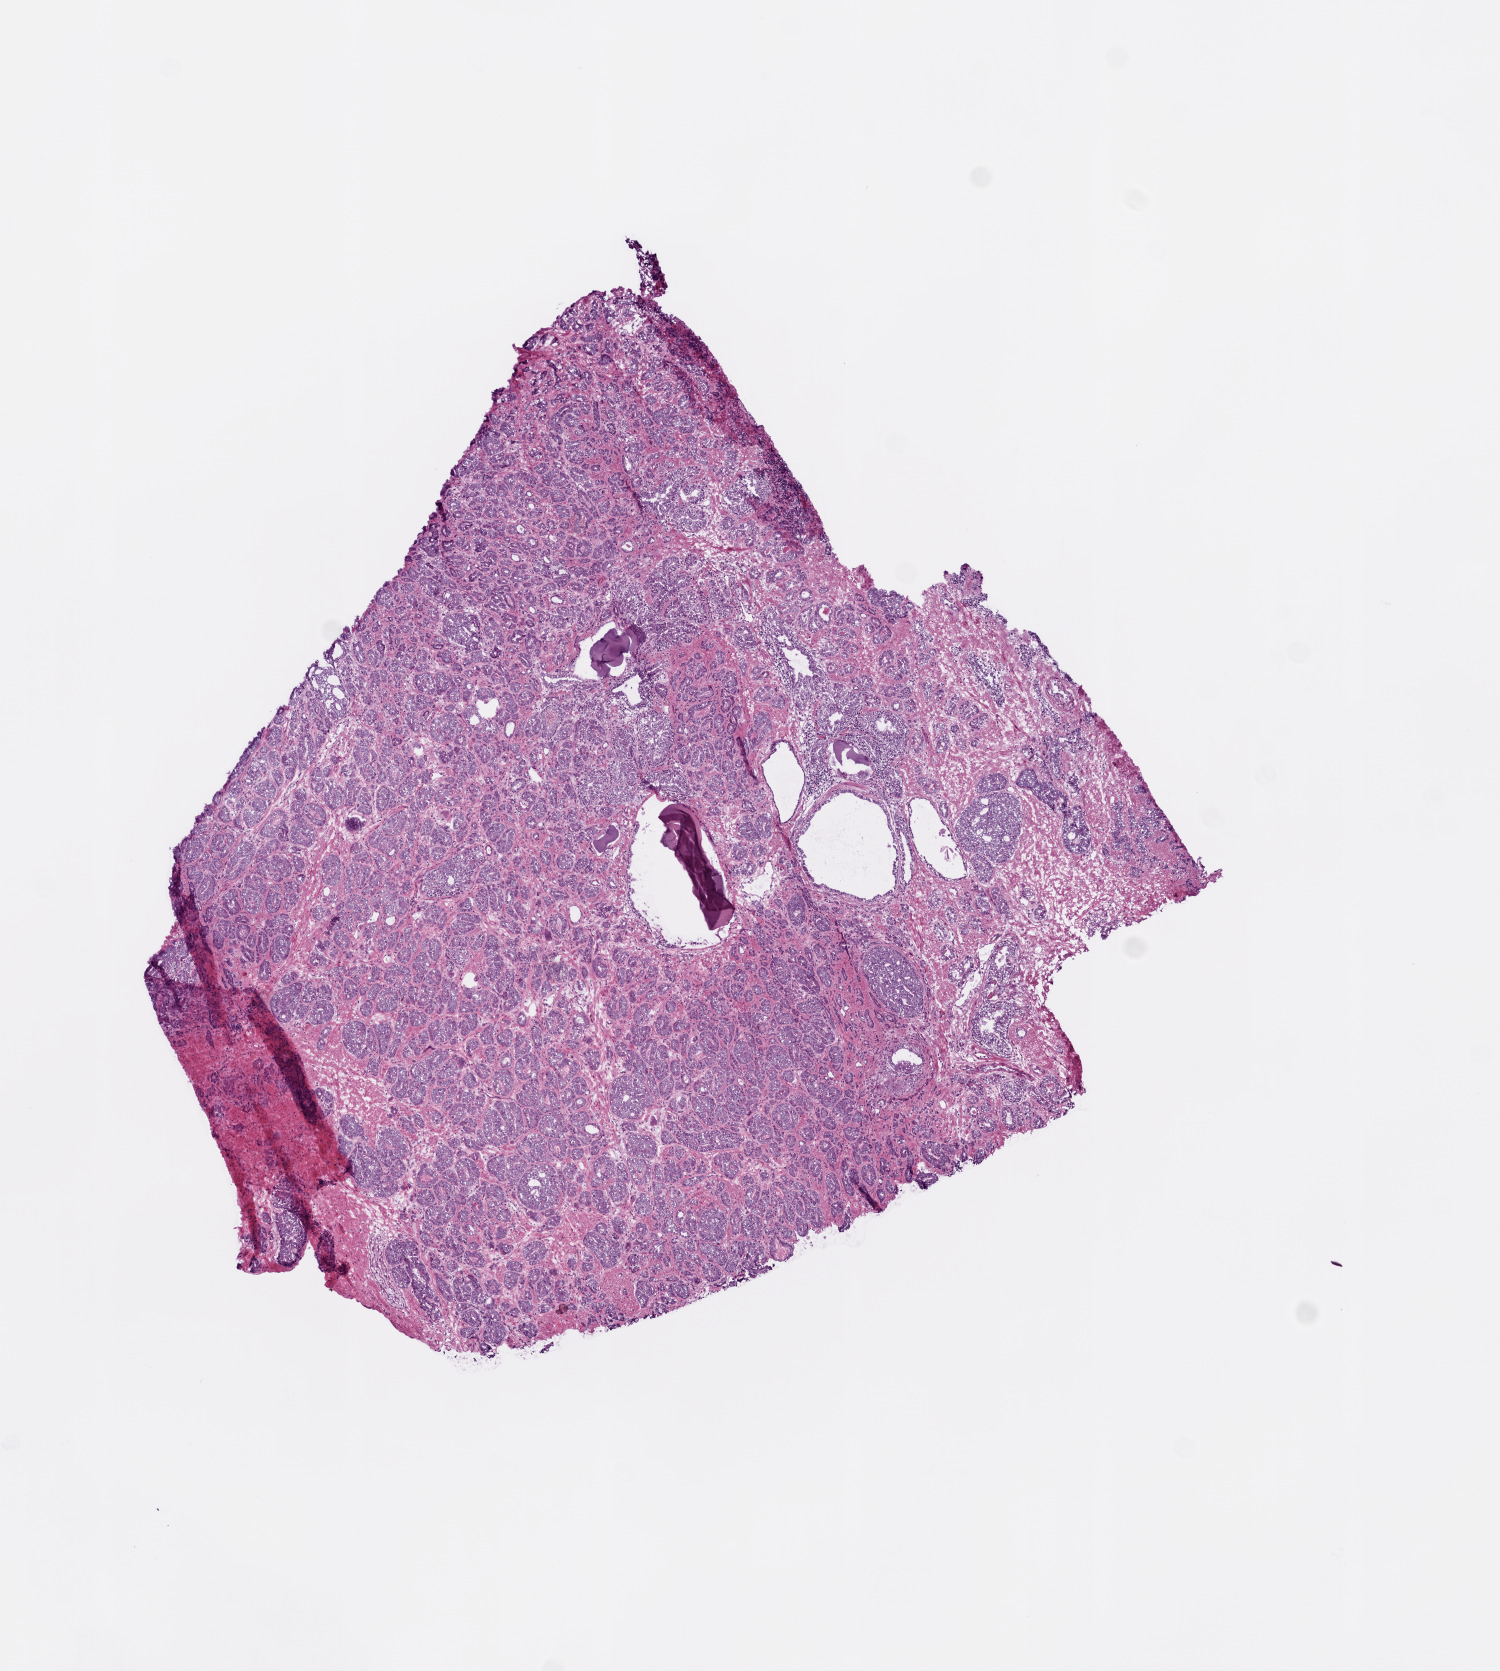
Digitized Hematoxylin and eosin (H&E) stained tissue section (whole slide) — shown as a low-resolution overview of the whole scanned area (about 6.0 x 6.7 mm, slide scanned at 20x); frozen section from the bottom of the tissue portion; primary tumour sample from the prostate. Male, age 60 years at initial diagnosis. Gleason score: 7 (4+3). Composition of this section per pathologist review: tumour cells 70%, tumour nuclei 80%, normal cells 15%, stromal cells 15%, necrosis 0%. Inflammatory infiltration, as recorded: lymphocyte infiltration 0%, monocyte infiltration 0%, neutrophil infiltration 0%.
Lymph nodes positive (case pathology): 0 of 7 examined. Pathologic diagnosis: Acinar cell carcinoma (prostate gland).